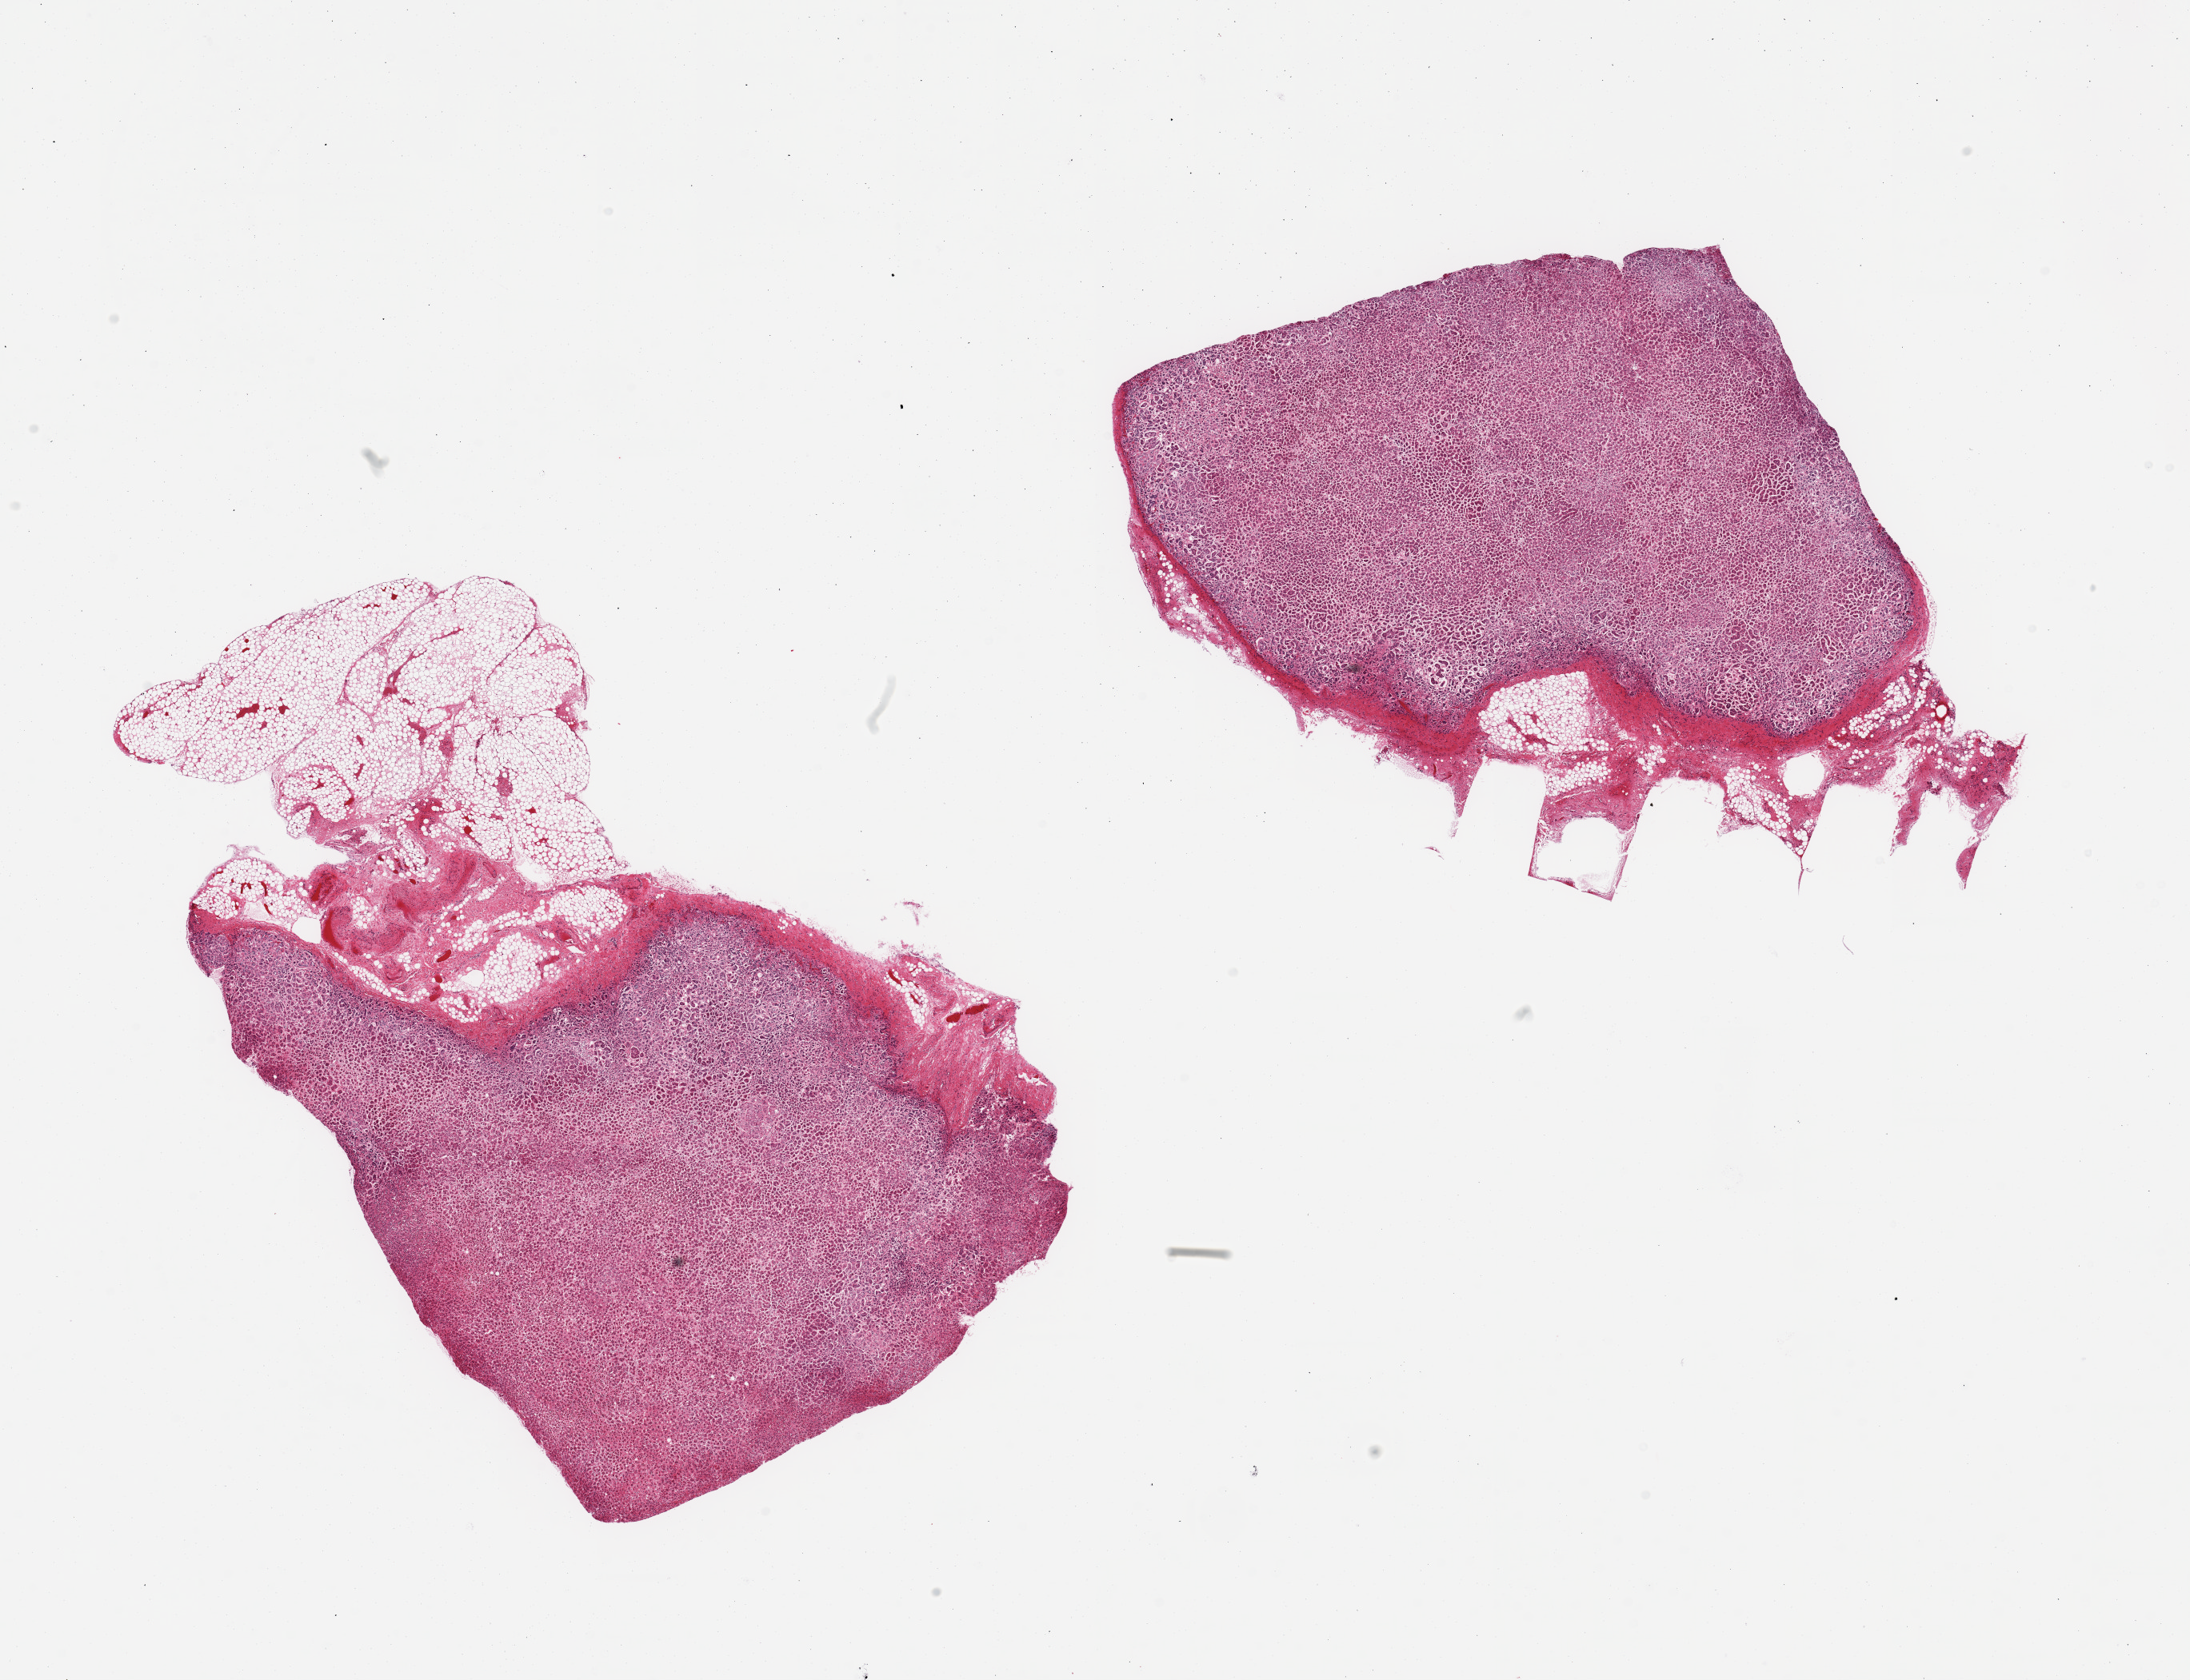
Whole-slide image, haematoxylin and eosin stain, low-resolution overview of the scanned area, about 21.7 x 16.6 mm. PAXgene-fixed paraffin-embedded (PFPE) section. Target tissue: adrenal gland. Tissue donor sample. Female donor.
- pathologist's review note for this sample: 2 pieces; well trimmed except for a 4mm fat nodule at end of 1 piece